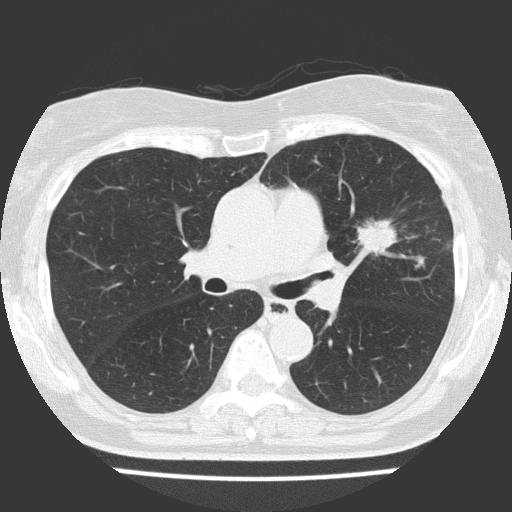
Low-dose screening chest CT, one axial slice; position 89 of 151 along the scan axis; lung window (W 1500 / L -600 HU); 2 mm slice thickness; 512 × 512 image matrix, field of view 309 × 309 mm.
Annotated regions visible in this slice (outlined manually by an expert reader):
- lesion 1 (tumor, upper lobe of left lung): bounding box [x1, y1, x2, y2] px = [357, 219, 397, 253]